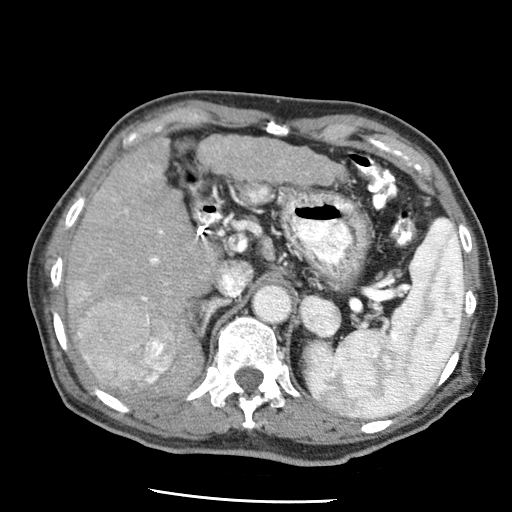
Contrast-enhanced abdominal CT (liver protocol), one axial slice. Slice 33 of 79 in the series (ordered by position). Reconstruction kernel STANDARD. 120 kVp. Soft-tissue window (W 400 / L 40 HU). 2.5 mm slice thickness. 512 × 512 image matrix, field of view 320 × 320 mm. Case-level facts recorded for this patient, not image findings: diagnosis: hepatocellular carcinoma (patient treated with transarterial chemoembolisation; whether this scan precedes or follows treatment is not stated here); TNM stage (as recorded): Stage-IIIA; Child-Pugh class: A; tumour differentiation: moderately differentiated; tumour nodularity: multinodular.
Outlined on this slice (semi-automatic segmentation, software-assisted and operator-edited):
- liver parenchyma outside the tumour (the mass and vessels are separate outlines, so this box may not span the whole liver): bounding box [x1, y1, x2, y2] px = [64, 138, 344, 396]
- mass: [68, 279, 177, 391]
- liver vessels: [112, 165, 207, 302]